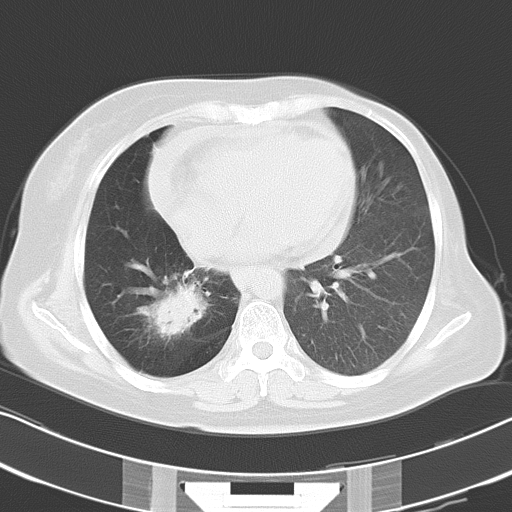
Chest CT, one axial slice. Position 13 of 30 along the scan axis. Reconstruction kernel B70f. Lung window (W 1500 / L -600 HU). 8 mm slice thickness. 512 × 512 image matrix. Patient: female, 53 years. From the clinical record (not read from this slice): clinical TNM (as recorded): T2b N1 M0.
Structures marked on this image (bounding box drawn by a radiologist):
- lung tumour (recorded histology: adenocarcinoma): box from (x=143, y=275) to (x=207, y=338) px